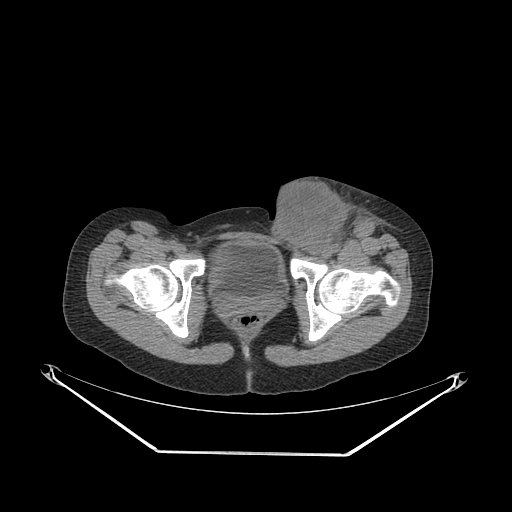
CT of an extremity soft-tissue mass (from a PET/CT study), one axial slice. Position 68 of 267 along the scan axis. Reconstruction kernel SOFT. Soft-tissue window (W 400 / L 40 HU). 3.75 mm slice thickness. 512 × 512 image matrix, field of view 500 × 500 mm. Female patient. From the clinical record (not read from this slice): histological type: leiomyosarcoma; grade: high; site of the primary tumour: groin.
Structures marked on this image (expert contour drawn on MRI and transferred to this co-registered scan by the dataset authors):
- gross tumour volume including surrounding oedema: bounding box (x1, y1, x2, y2) in pixels: (267, 181, 382, 257)
- gross tumour volume (mass): (267, 185, 348, 254)